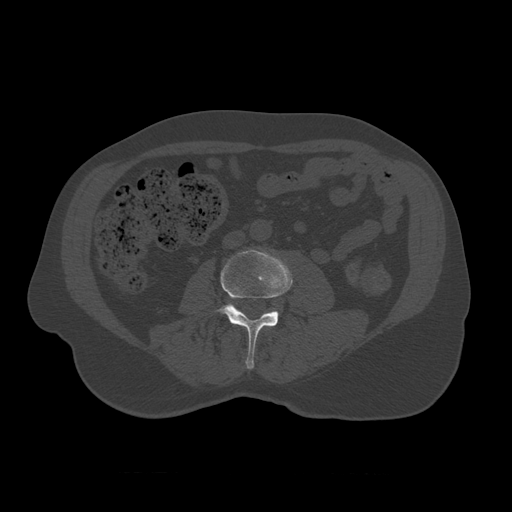
CT including the spine, one axial slice; slice 299 of 450 in the series (ordered by position); bone window (W 1800 / L 400 HU); 1.25 mm slice thickness; 512 × 512 image matrix, field of view 405 × 405 mm. Patient age 75 years. Case-level facts recorded for this patient, not image findings: primary cancer: prostate.
Structures marked on this image (semi-automatic segmentation, software-assisted and operator-edited):
- L3 vertebra: bounding box (x1, y1, x2, y2) in pixels: (215, 249, 293, 370)